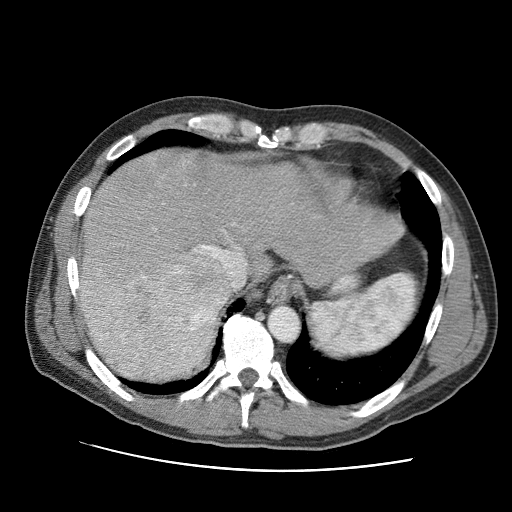
Contrast-enhanced abdominal CT (liver protocol), one axial slice; slice 78 of 95 in the series (ordered by position); reconstruction kernel STANDARD; 120 kVp; one of 2 acquisitions stored at this slice position; soft-tissue window (W 400 / L 40 HU); 2.5 mm slice thickness; 512 × 512 image matrix. Case-level facts recorded for this patient, not image findings: diagnosis: hepatocellular carcinoma (patient treated with transarterial chemoembolisation; whether this scan precedes or follows treatment is not stated here); TNM stage (as recorded): Stage-IVA; Child-Pugh class: A; tumour differentiation: moderately differentiated.
Outlined on this slice (semi-automatic segmentation, software-assisted and operator-edited):
- liver parenchyma outside the tumour (the mass and vessels are separate outlines, so this box may not span the whole liver): bounding box (x1, y1, x2, y2) in pixels: (80, 150, 402, 370)
- mass: (80, 241, 228, 382)
- liver vessels: (221, 223, 245, 288)